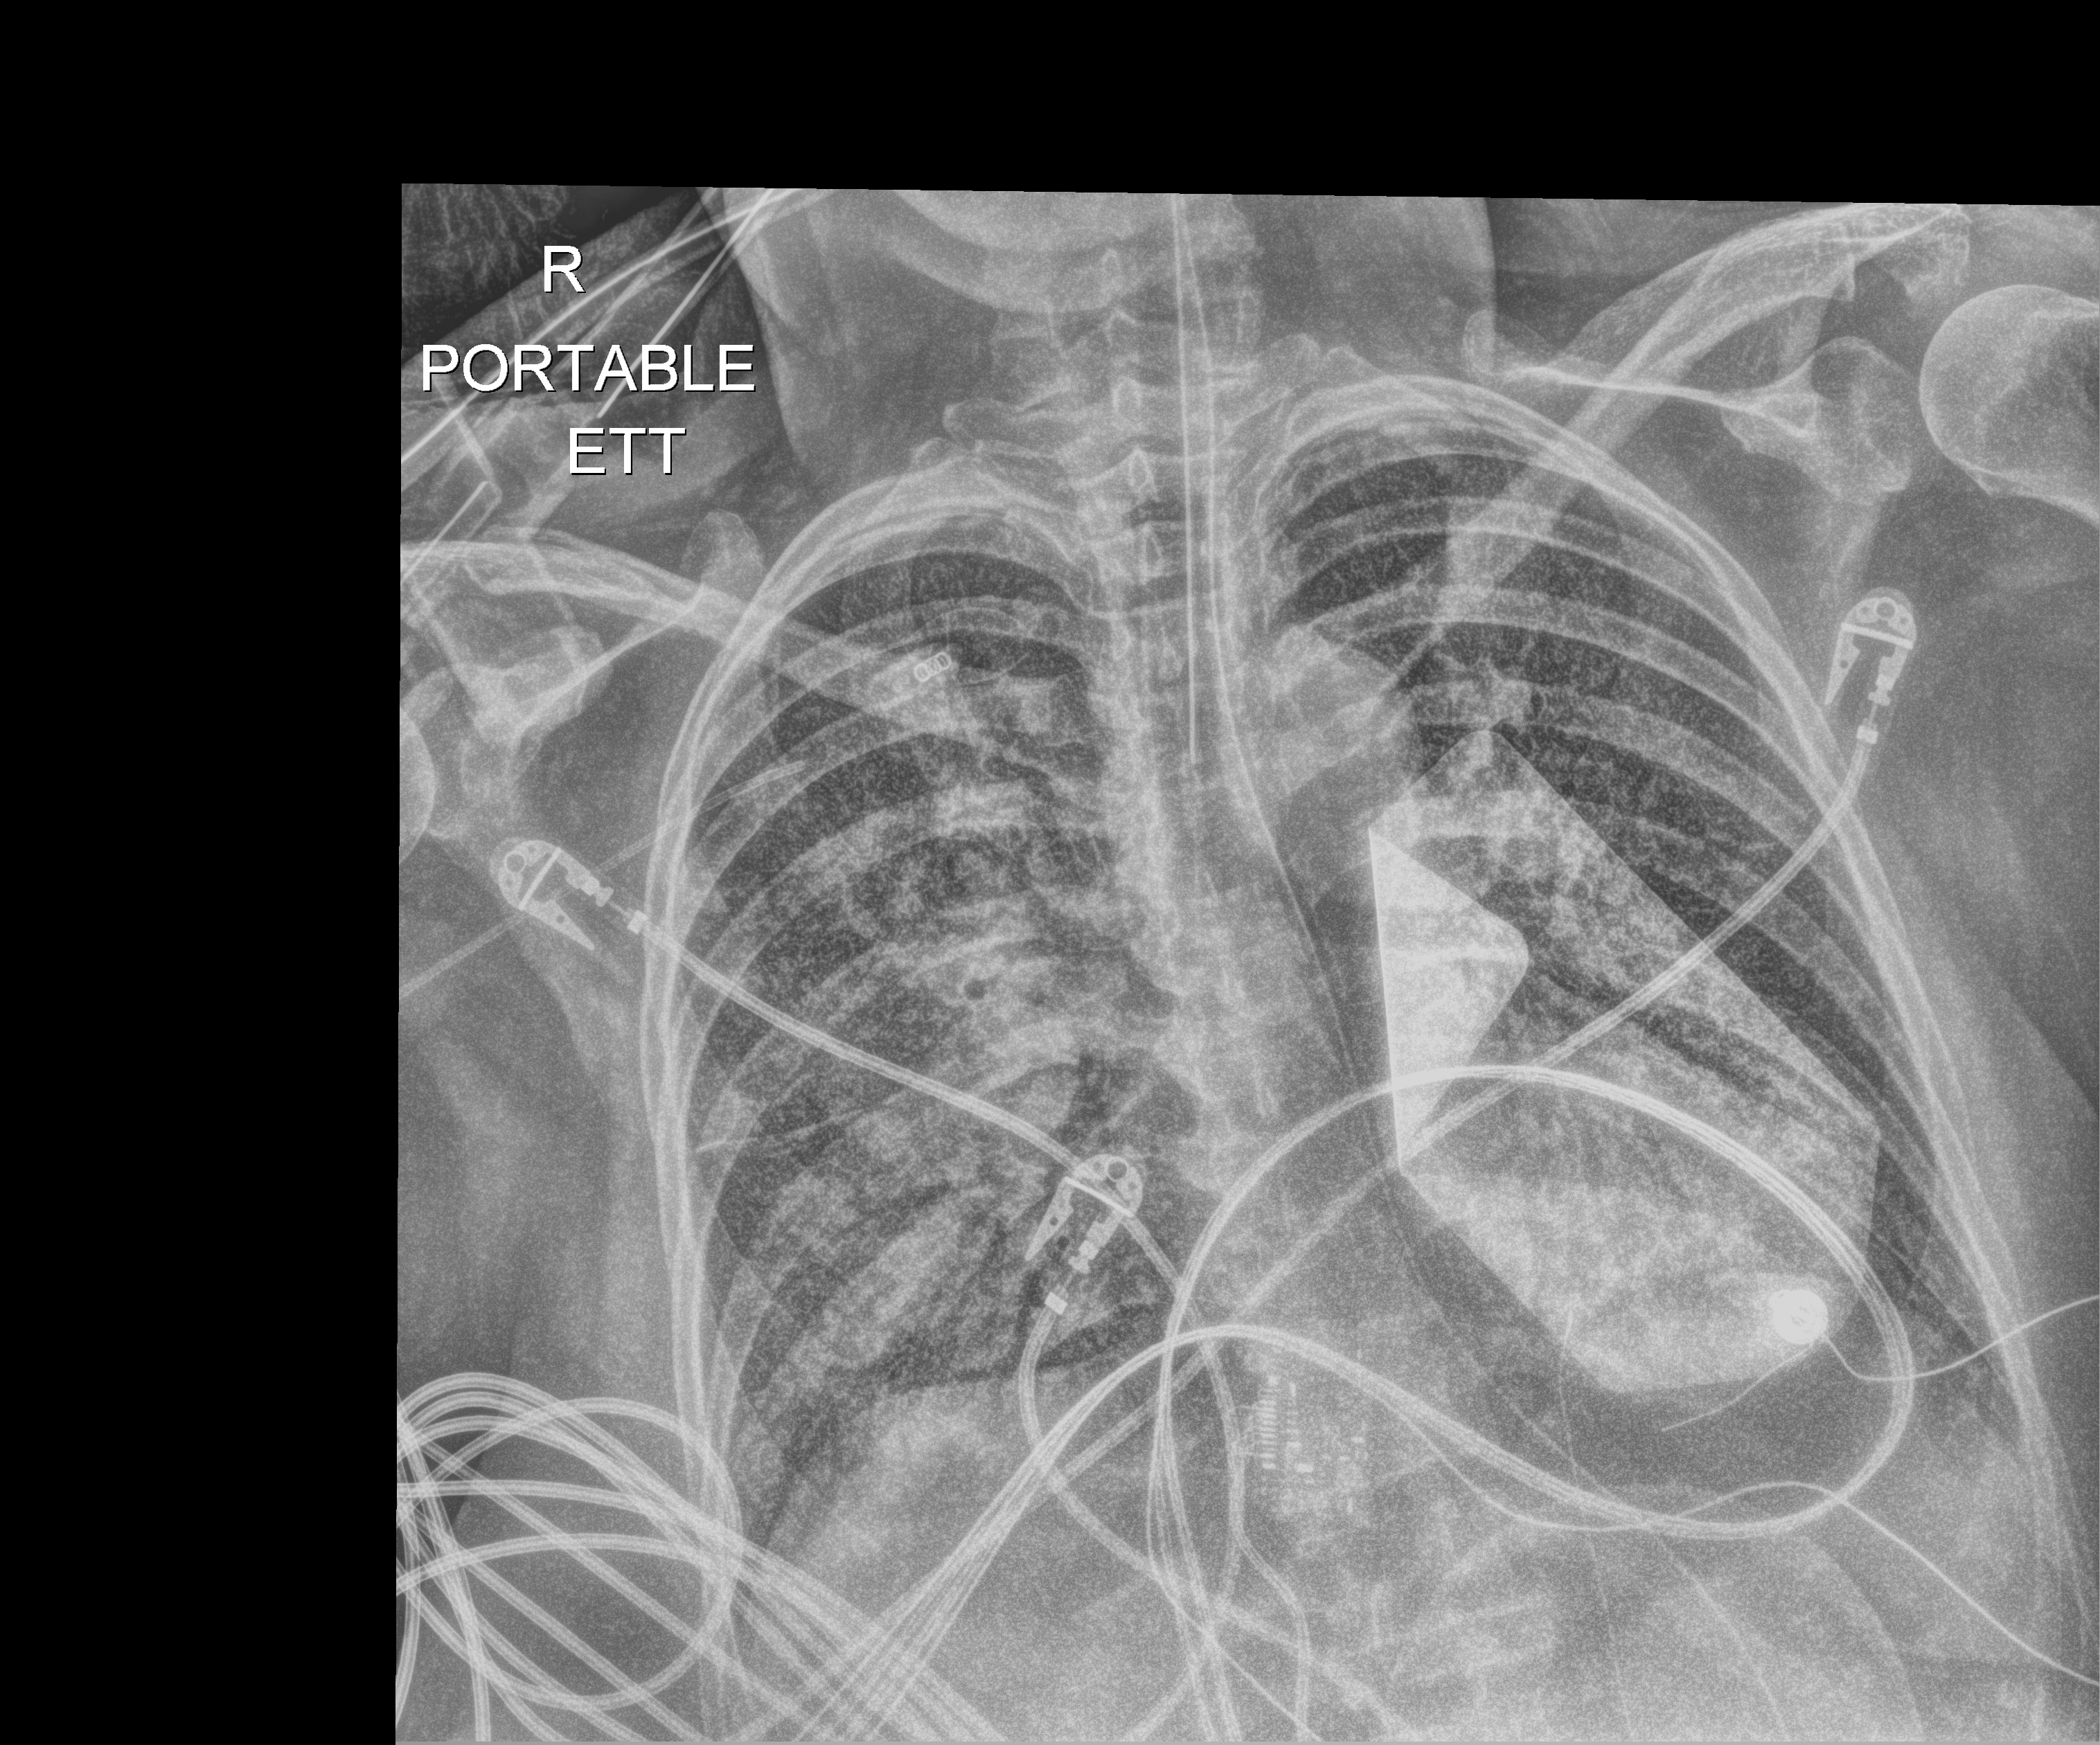
Bedside chest radiograph (digital radiography), anteroposterior (AP) projection. Female patient hospitalised with COVID-19, age 60–74 years.
Admission-level facts for this patient (not findings on this image; timing relative to this image not recorded): length of hospital stay: 38 days; diabetes (admission record): no.